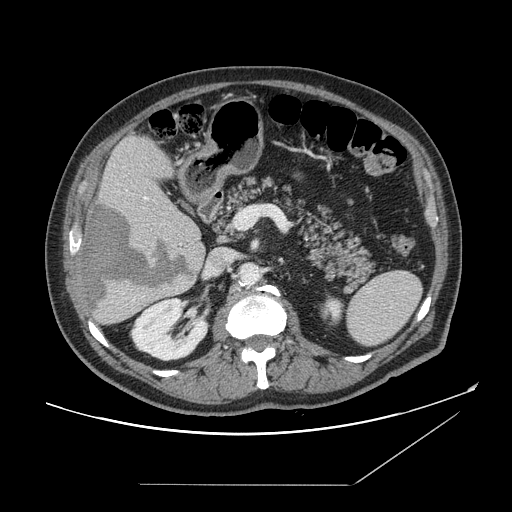
Contrast-enhanced abdominal CT, one axial slice. Position 80 of 166 along the scan axis. Intravenous contrast given. Soft-tissue window (W 400 / L 40 HU). 2.5 mm slice thickness. 512 × 512 image matrix, field of view 416 × 416 mm. Male patient, age 80 years. Case-level facts recorded for this patient, not image findings: diagnosis: colorectal cancer liver metastases, imaged before liver resection; multiple liver metastases: no; largest metastasis: 2.2 cm; disease in both lobes: no.
Structures marked on this image (expert manual segmentation):
- hepatic veins: bounding box <146,197,148,200> (left, top, right, bottom; pixels)
- liver: <78,136,206,326>
- planned liver remnant (the part of the liver to remain after resection): <102,135,200,236>
- liver metastasis: <82,202,195,312>